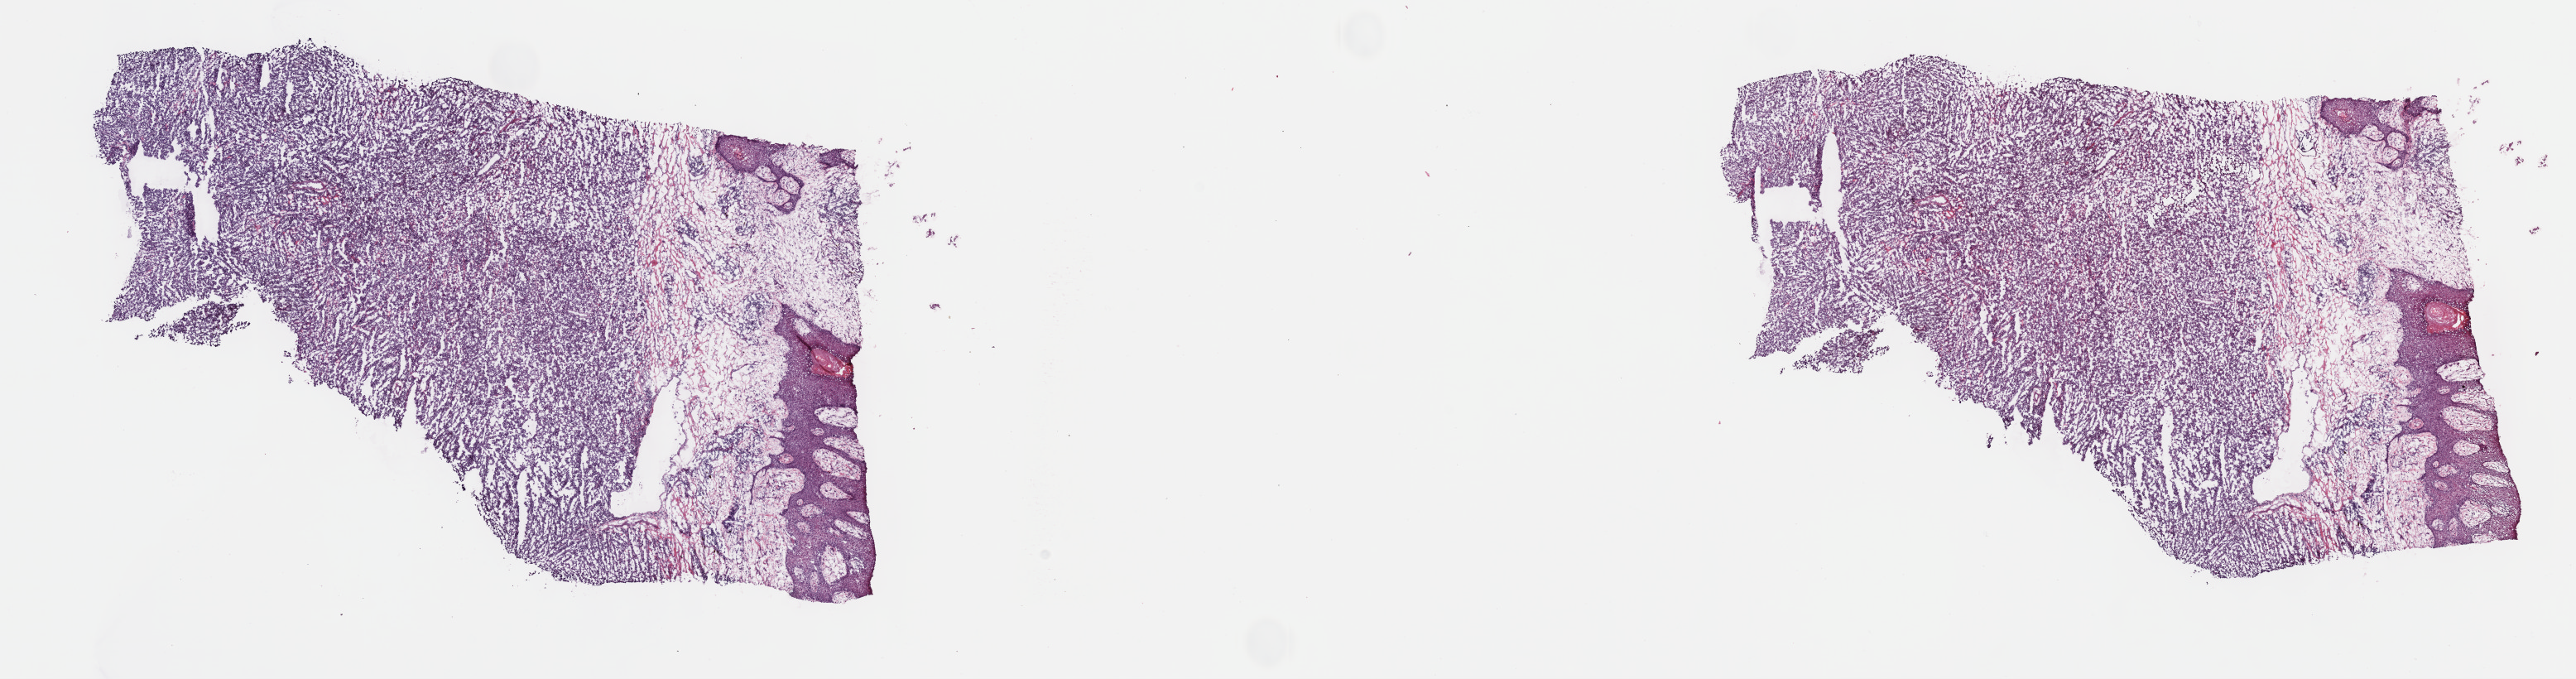
Whole-slide histology image, H&E, whole scanned area (about 25.2 x 6.6 mm, from a 40x scan) shown as a low-resolution overview. Frozen section. Primary tumour sample from the skin. Male, age 83 years at initial diagnosis.
Pathologic diagnosis: Epithelioid cell melanoma.